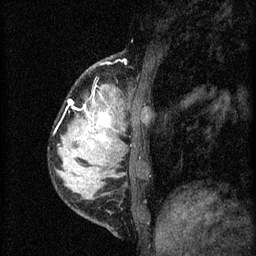
Breast MRI (dynamic contrast-enhanced), one sagittal slice; slice 14 of 60 in the series (ordered by position); 3 images stored at this slice position (order not interpretable as contrast timing); 1.5 T; TE 4.2 ms, TR 8.2 ms; 256 × 256 image matrix, field of view 180 × 180 mm. Female patient, age 37 years.
Annotated regions visible in this slice (semi-automatic segmentation, software-assisted and operator-edited):
- analysis volume of interest (the breast-tissue region the enhancement analysis was run in; not a lesion): bounding box <56,82,140,181> (left, top, right, bottom; pixels)
- tumour enhancement mask (voxels above the 70 % enhancement threshold inside the analysis volume of interest): <69,100,111,147>